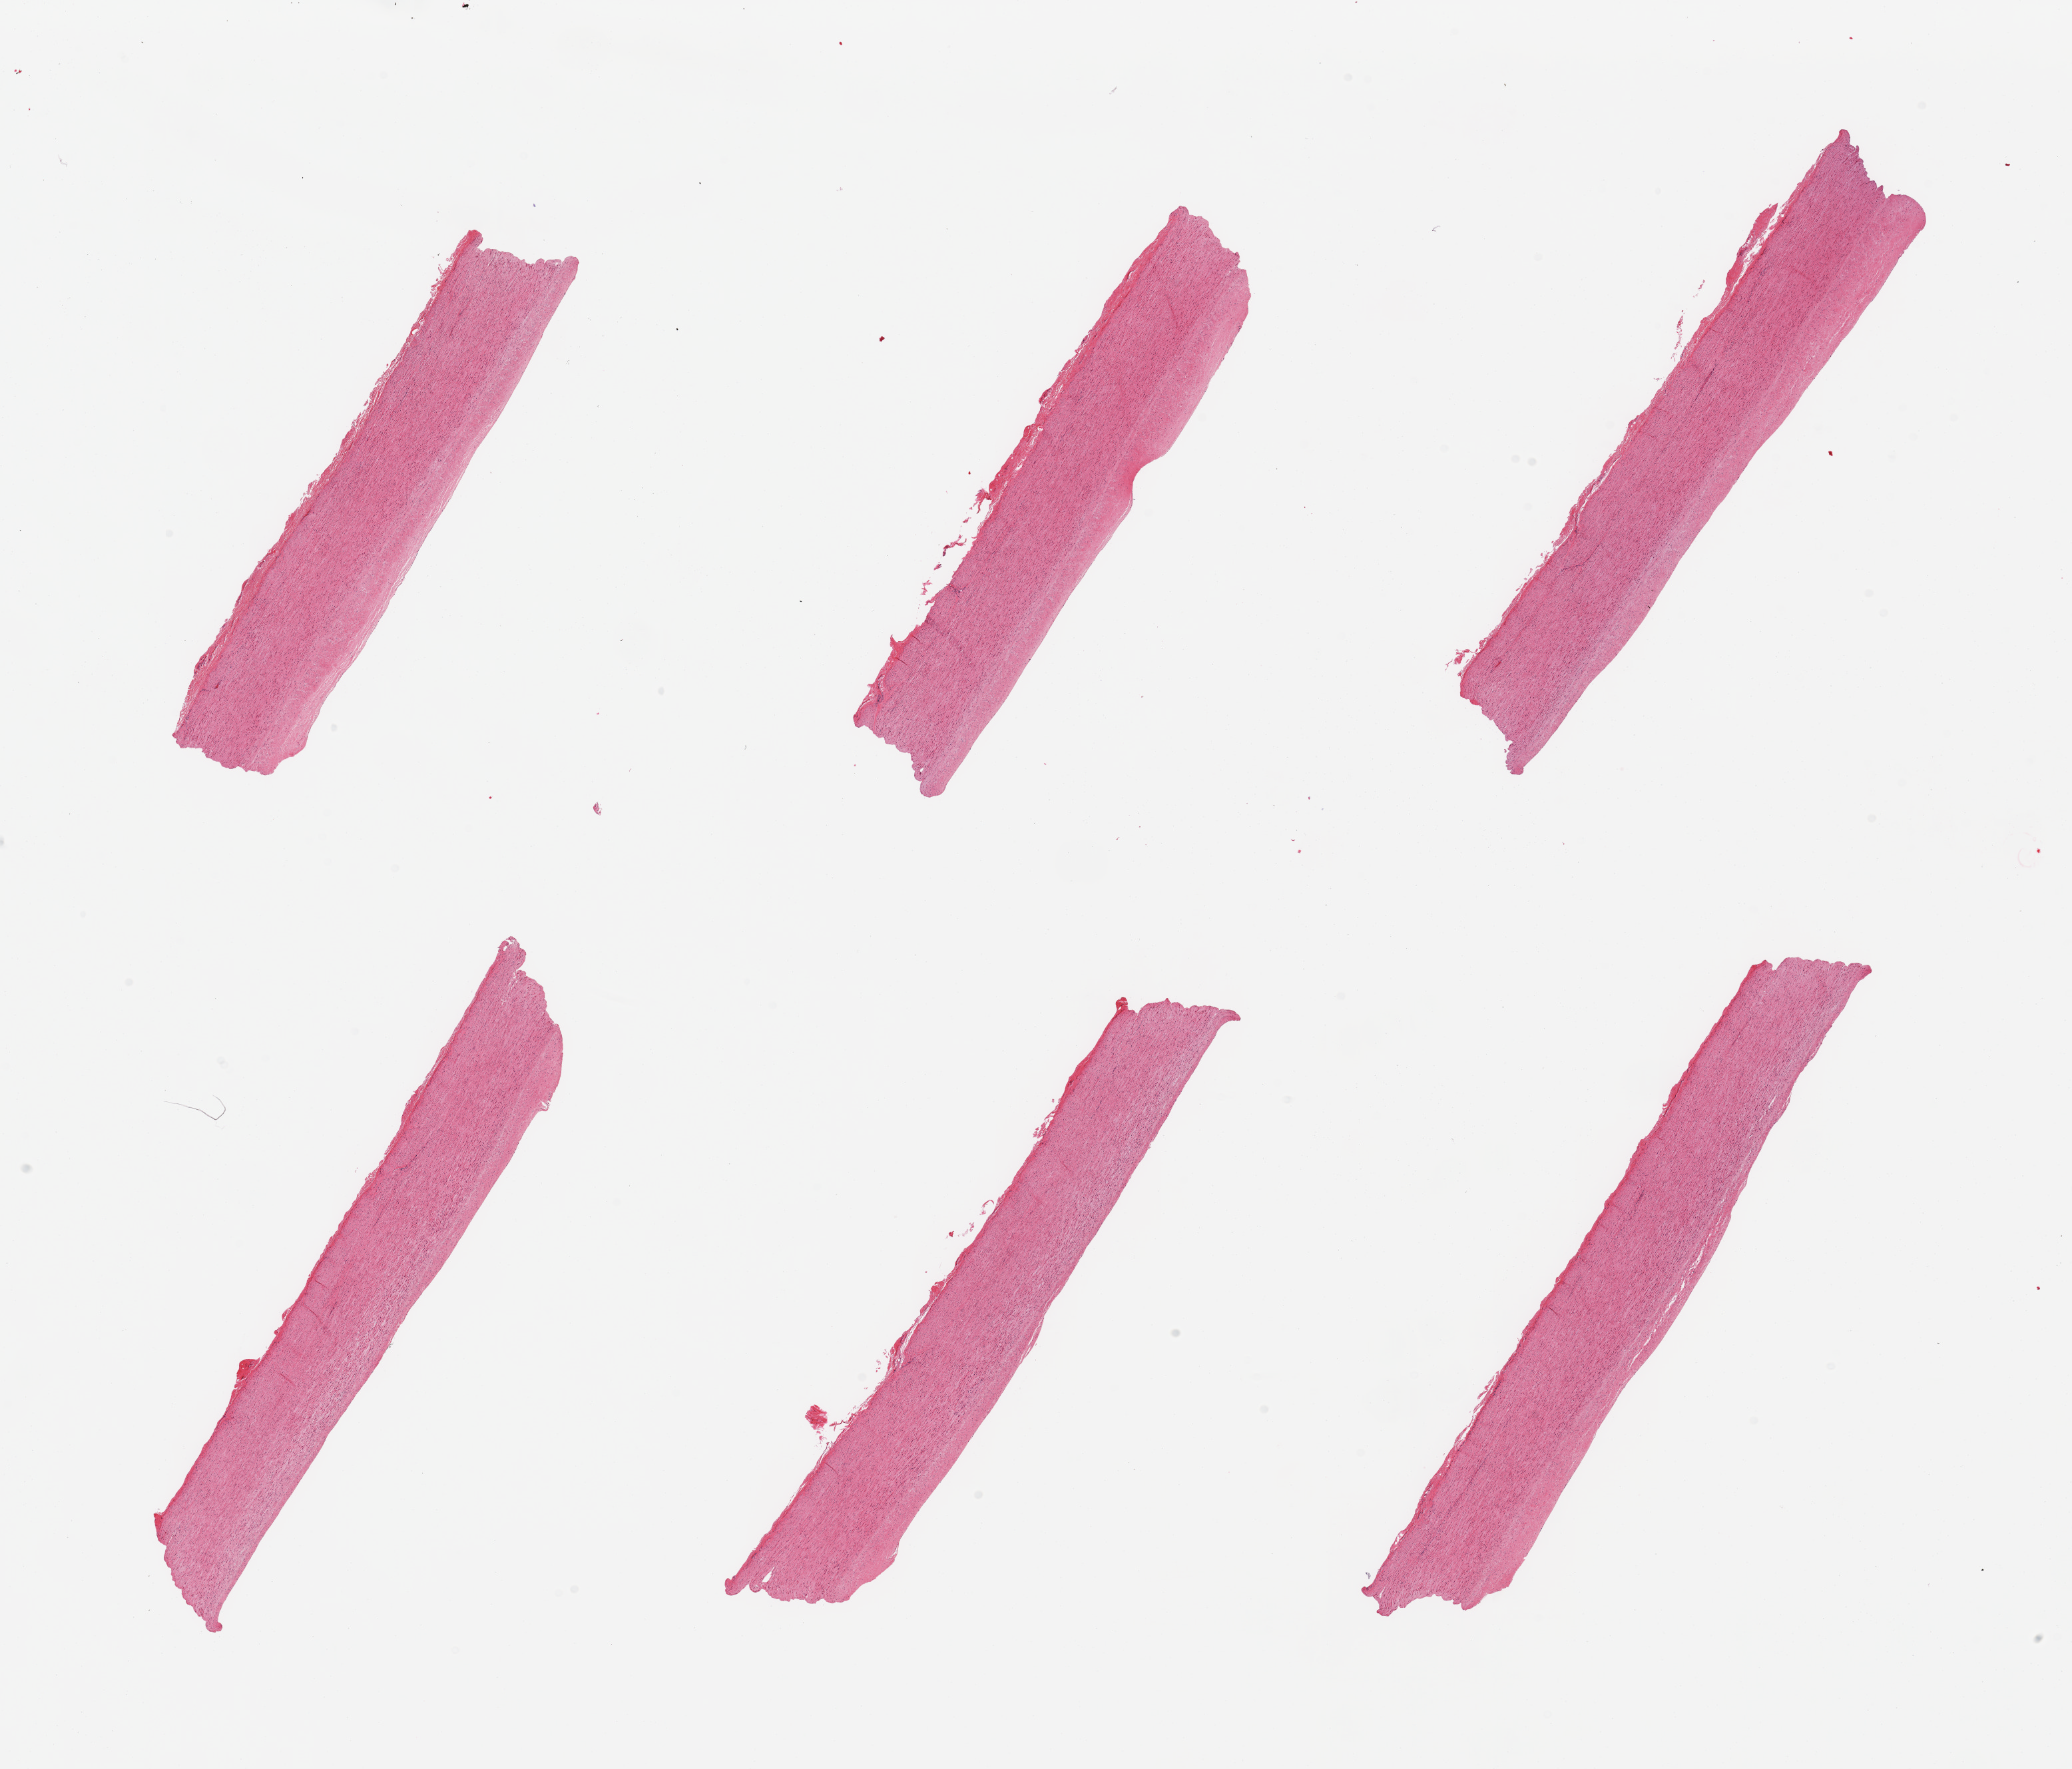
Digitized hematoxylin and eosin (H&E)-stained section, shown as a low-resolution overview of the whole scanned area (about 24.6 x 21.0 mm, slide scanned at 20x). PAXgene-fixed paraffin-embedded (PFPE) section. Sampled site (target tissue): aorta. Donor tissue sample. Male donor.
Reviewer comment on this tissue sample: 6 pieces; mild flat fibrous plaques; well trimmed.